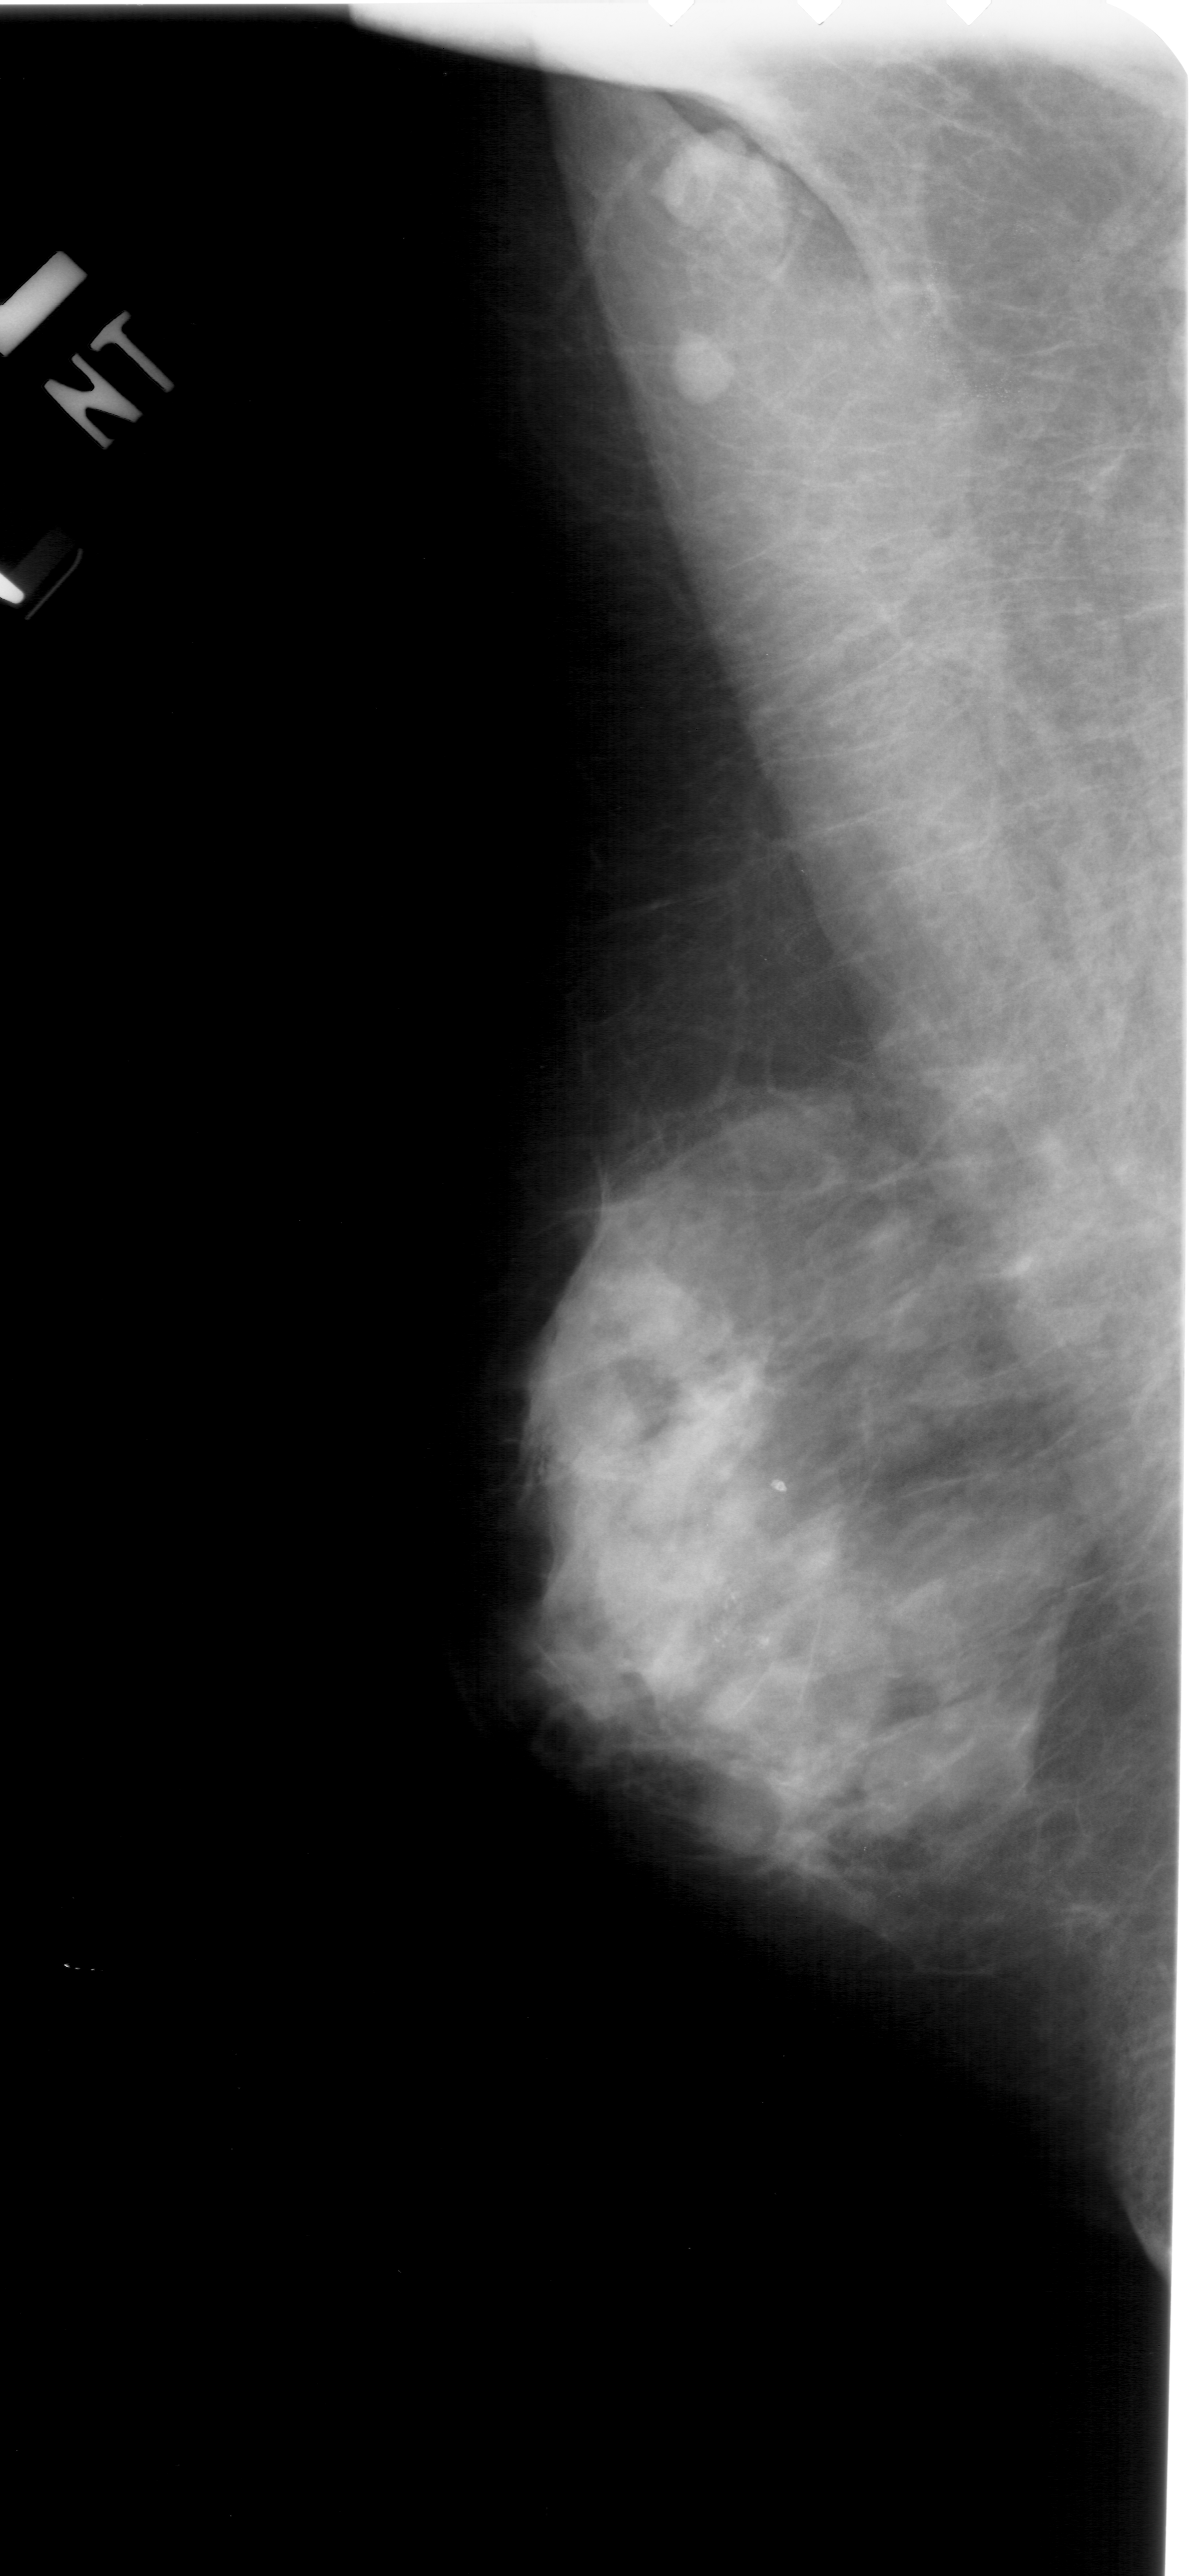
Scanned film-screen mammogram, left breast, mediolateral oblique (MLO) view.
Calcifications, morphology pleomorphic, distribution clustered; BI-RADS assessment category 4; pathology result (as recorded, not read from the image): malignant.